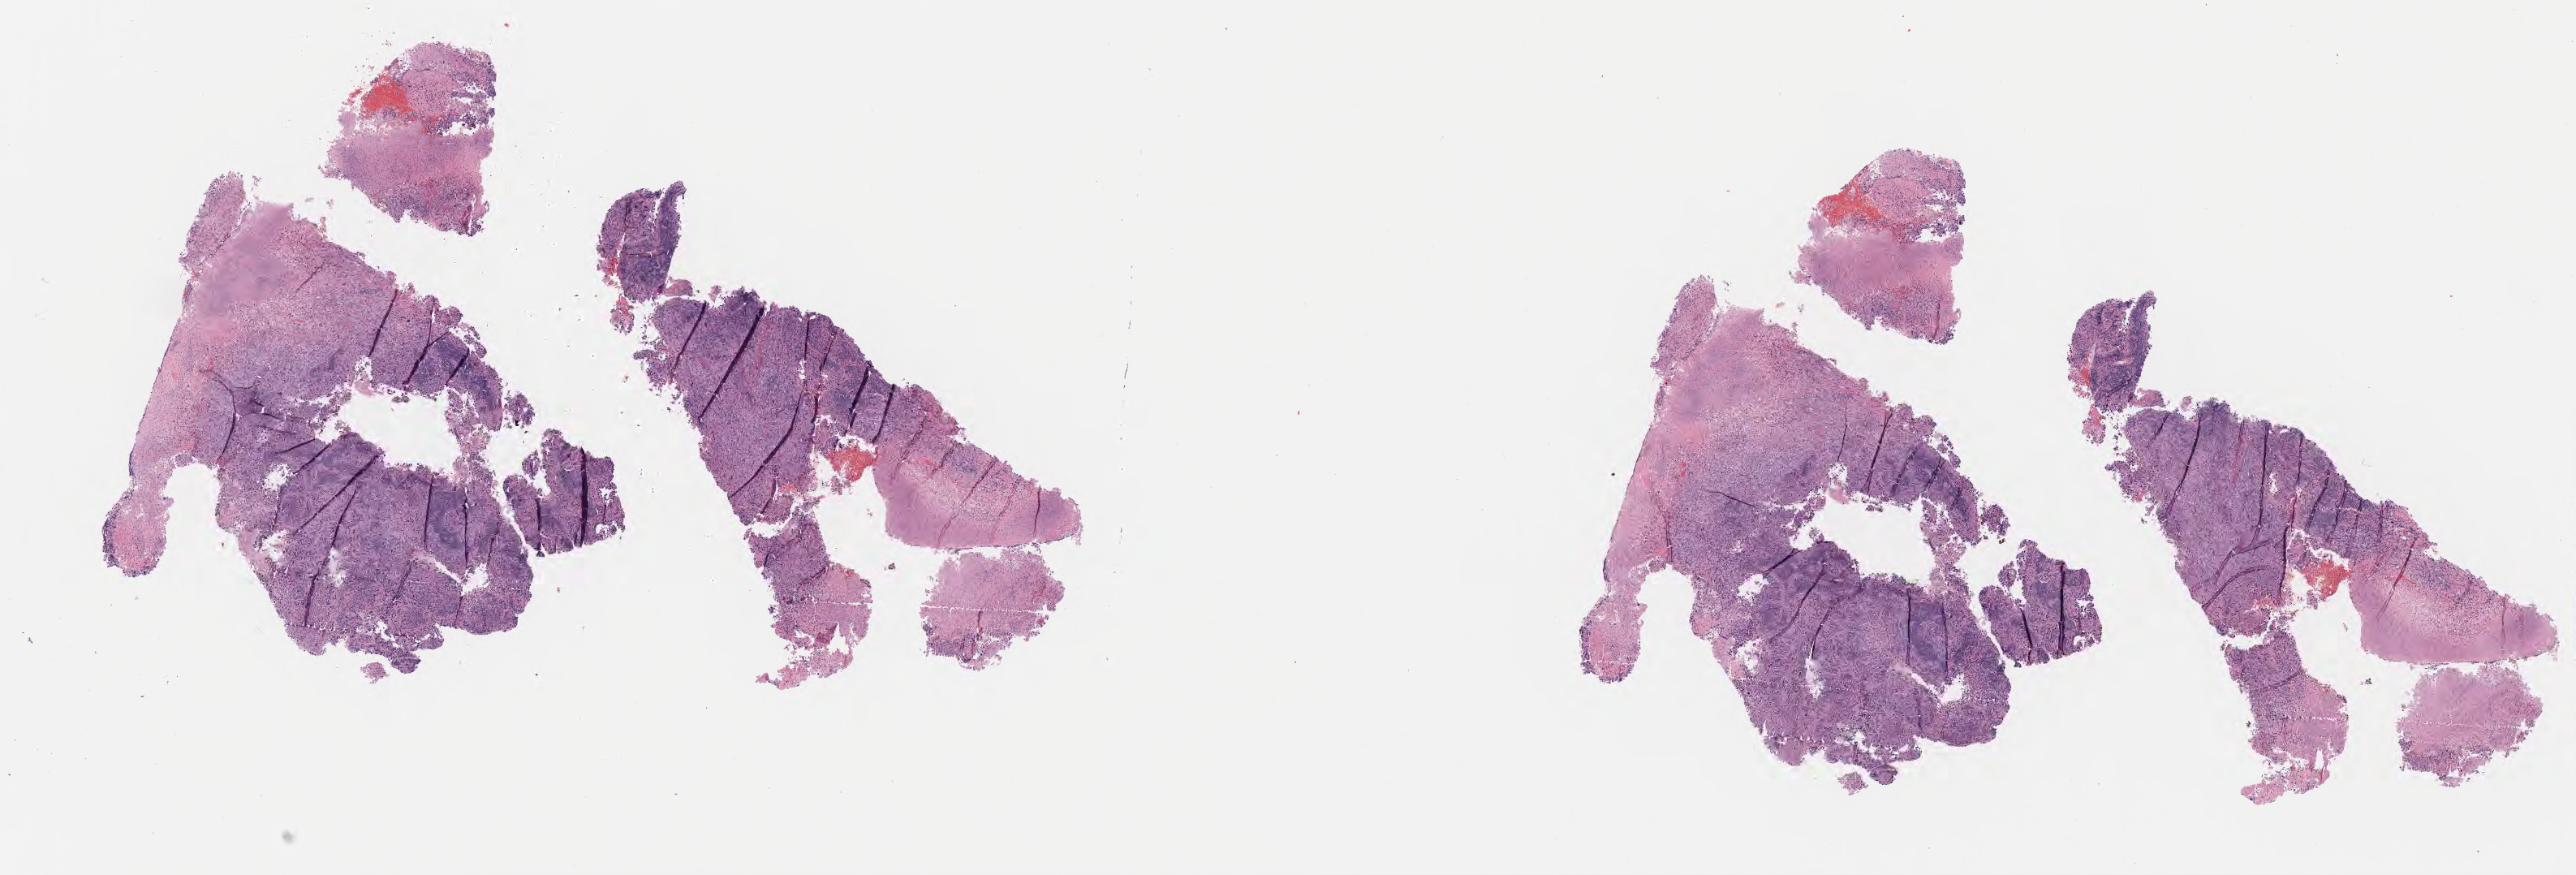
Whole-slide image, hematoxylin and eosin (H&E) stain — low-resolution overview of the scanned area, about 25.7 x 8.7 mm; tumor tissue; anatomic site: cervix. Patient: female, aged 38.
Diagnosis: Squamous cell carcinoma, large cell, nonkeratinizing, NOS.